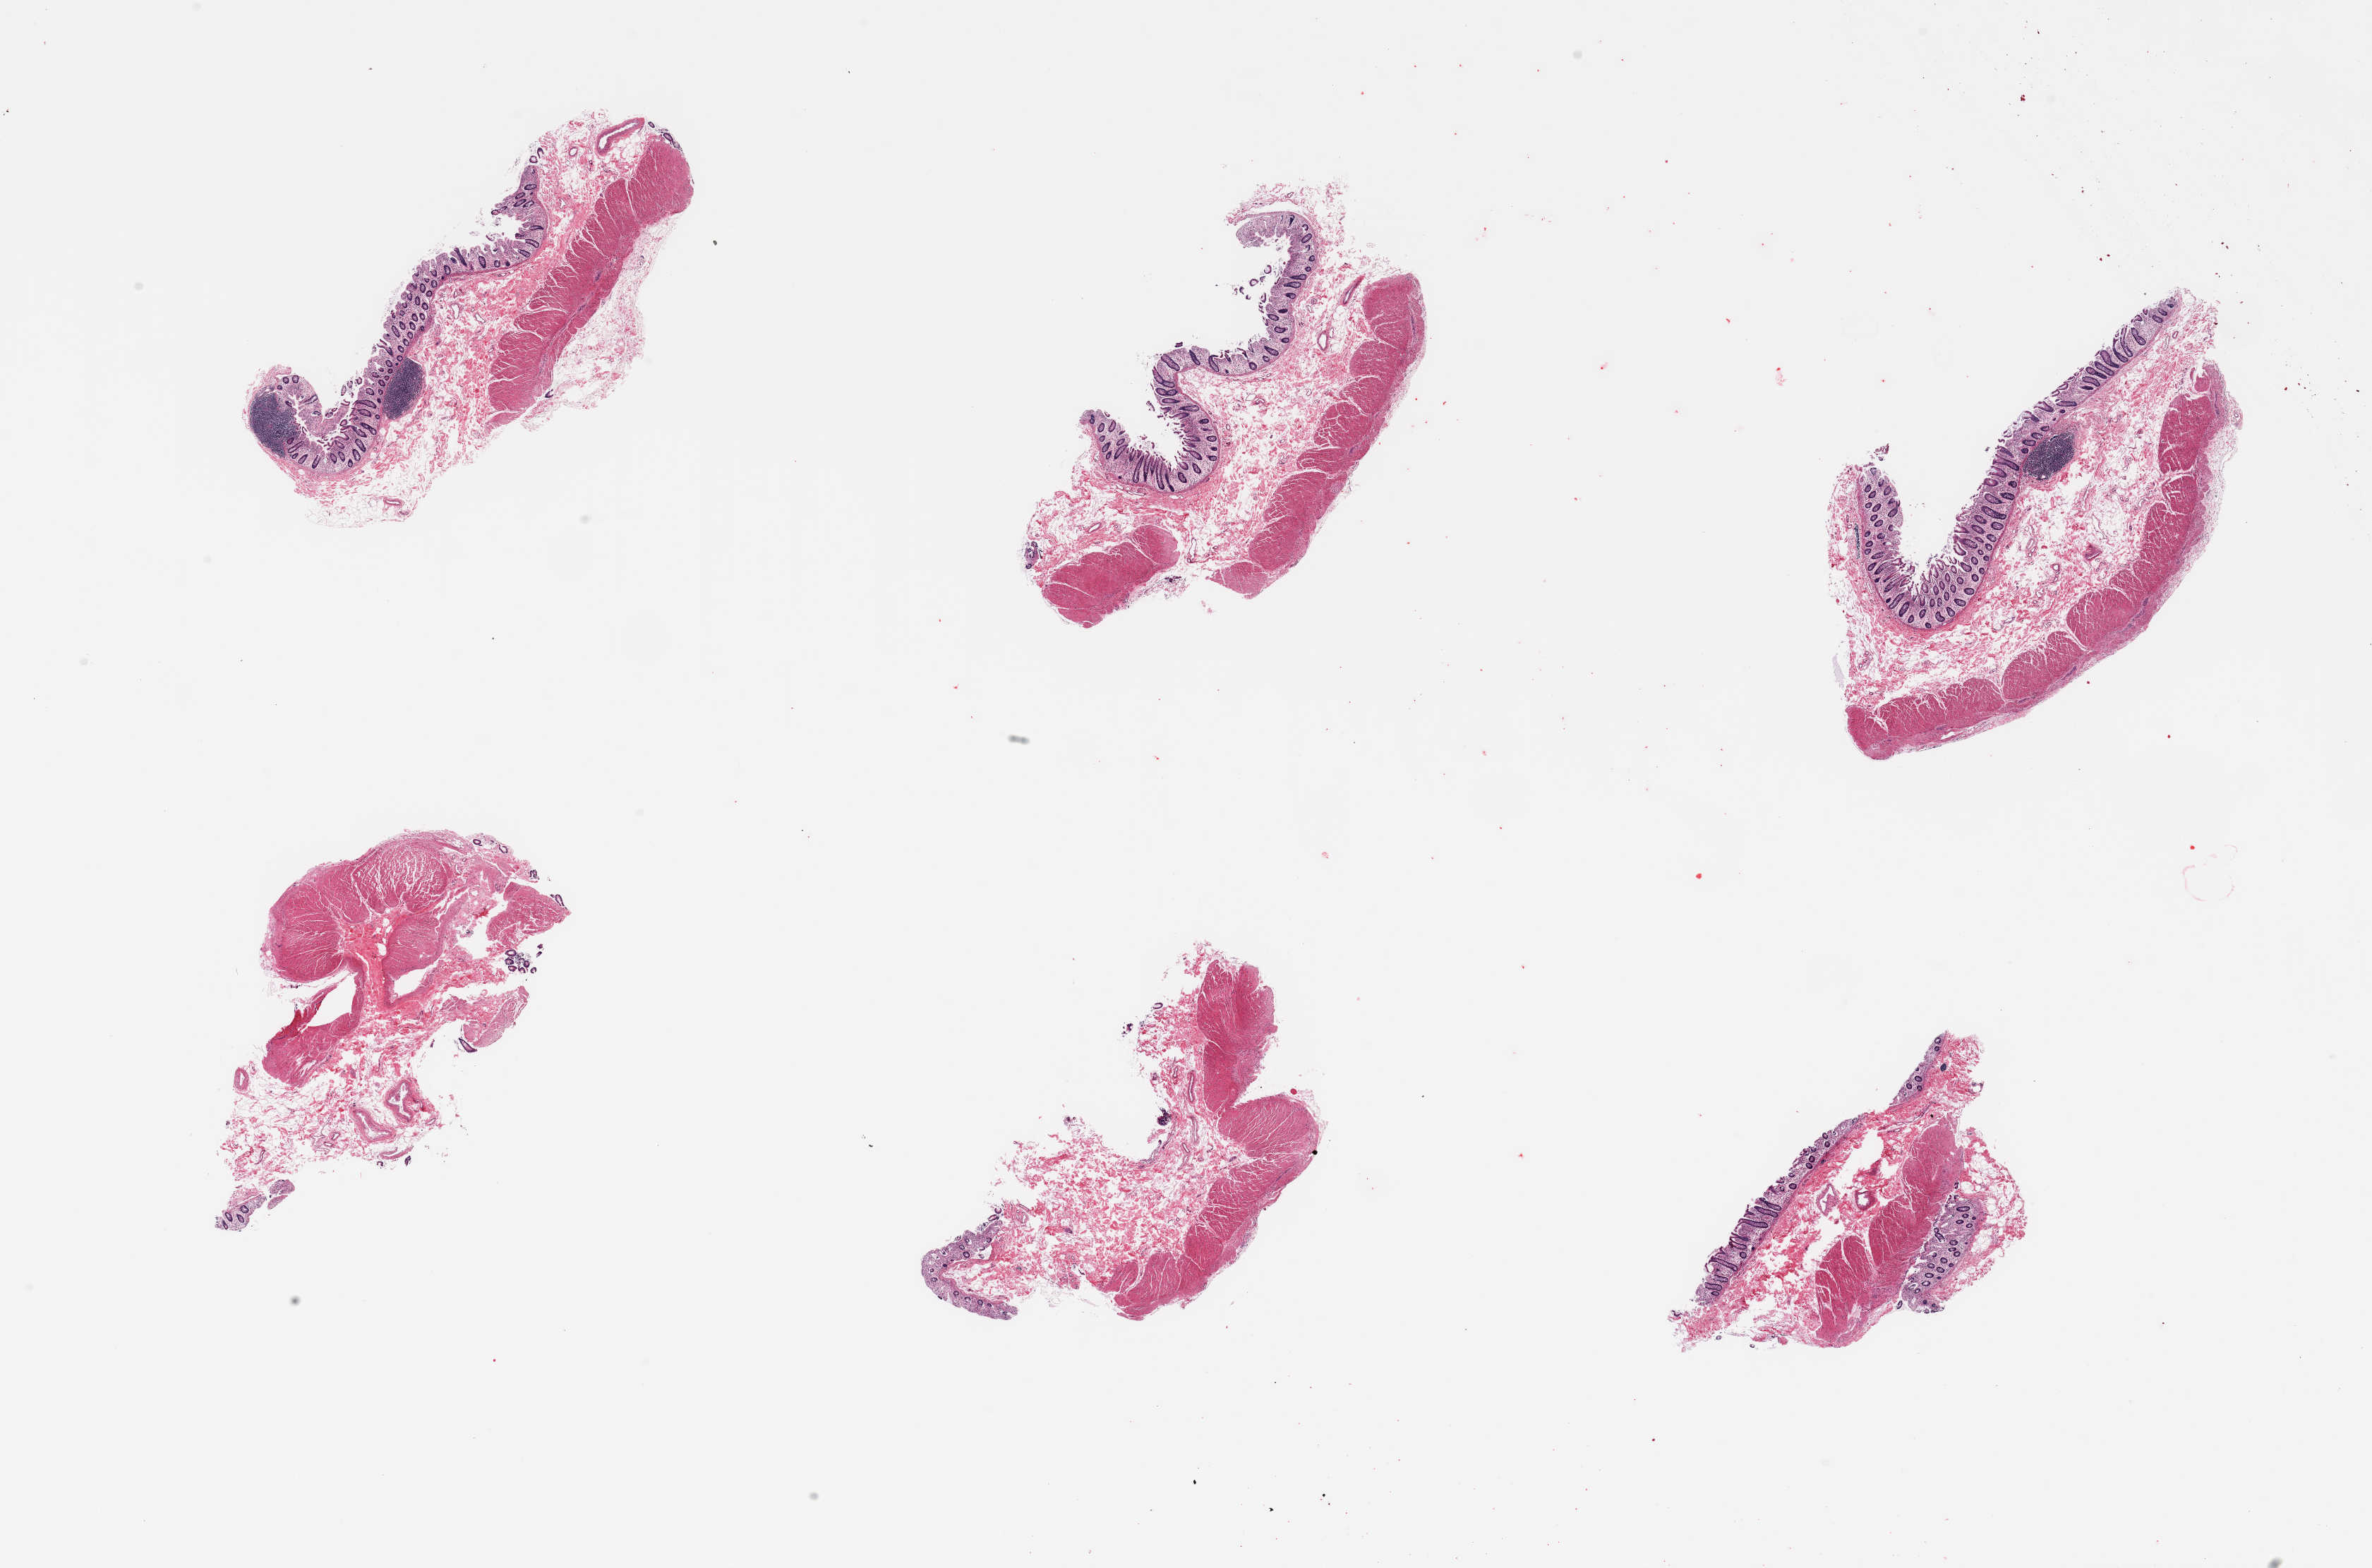
Whole-slide image, haematoxylin and eosin stain, brightfield, shown as a low-resolution overview of the whole scanned area (about 26.6 x 17.6 mm). PAXgene-fixed, paraffin-embedded tissue. Section of transverse colon (target tissue). Donor tissue sample.
Pathologist's review note for this sample: 6 pieces; variable amounts of mucosa sampled.